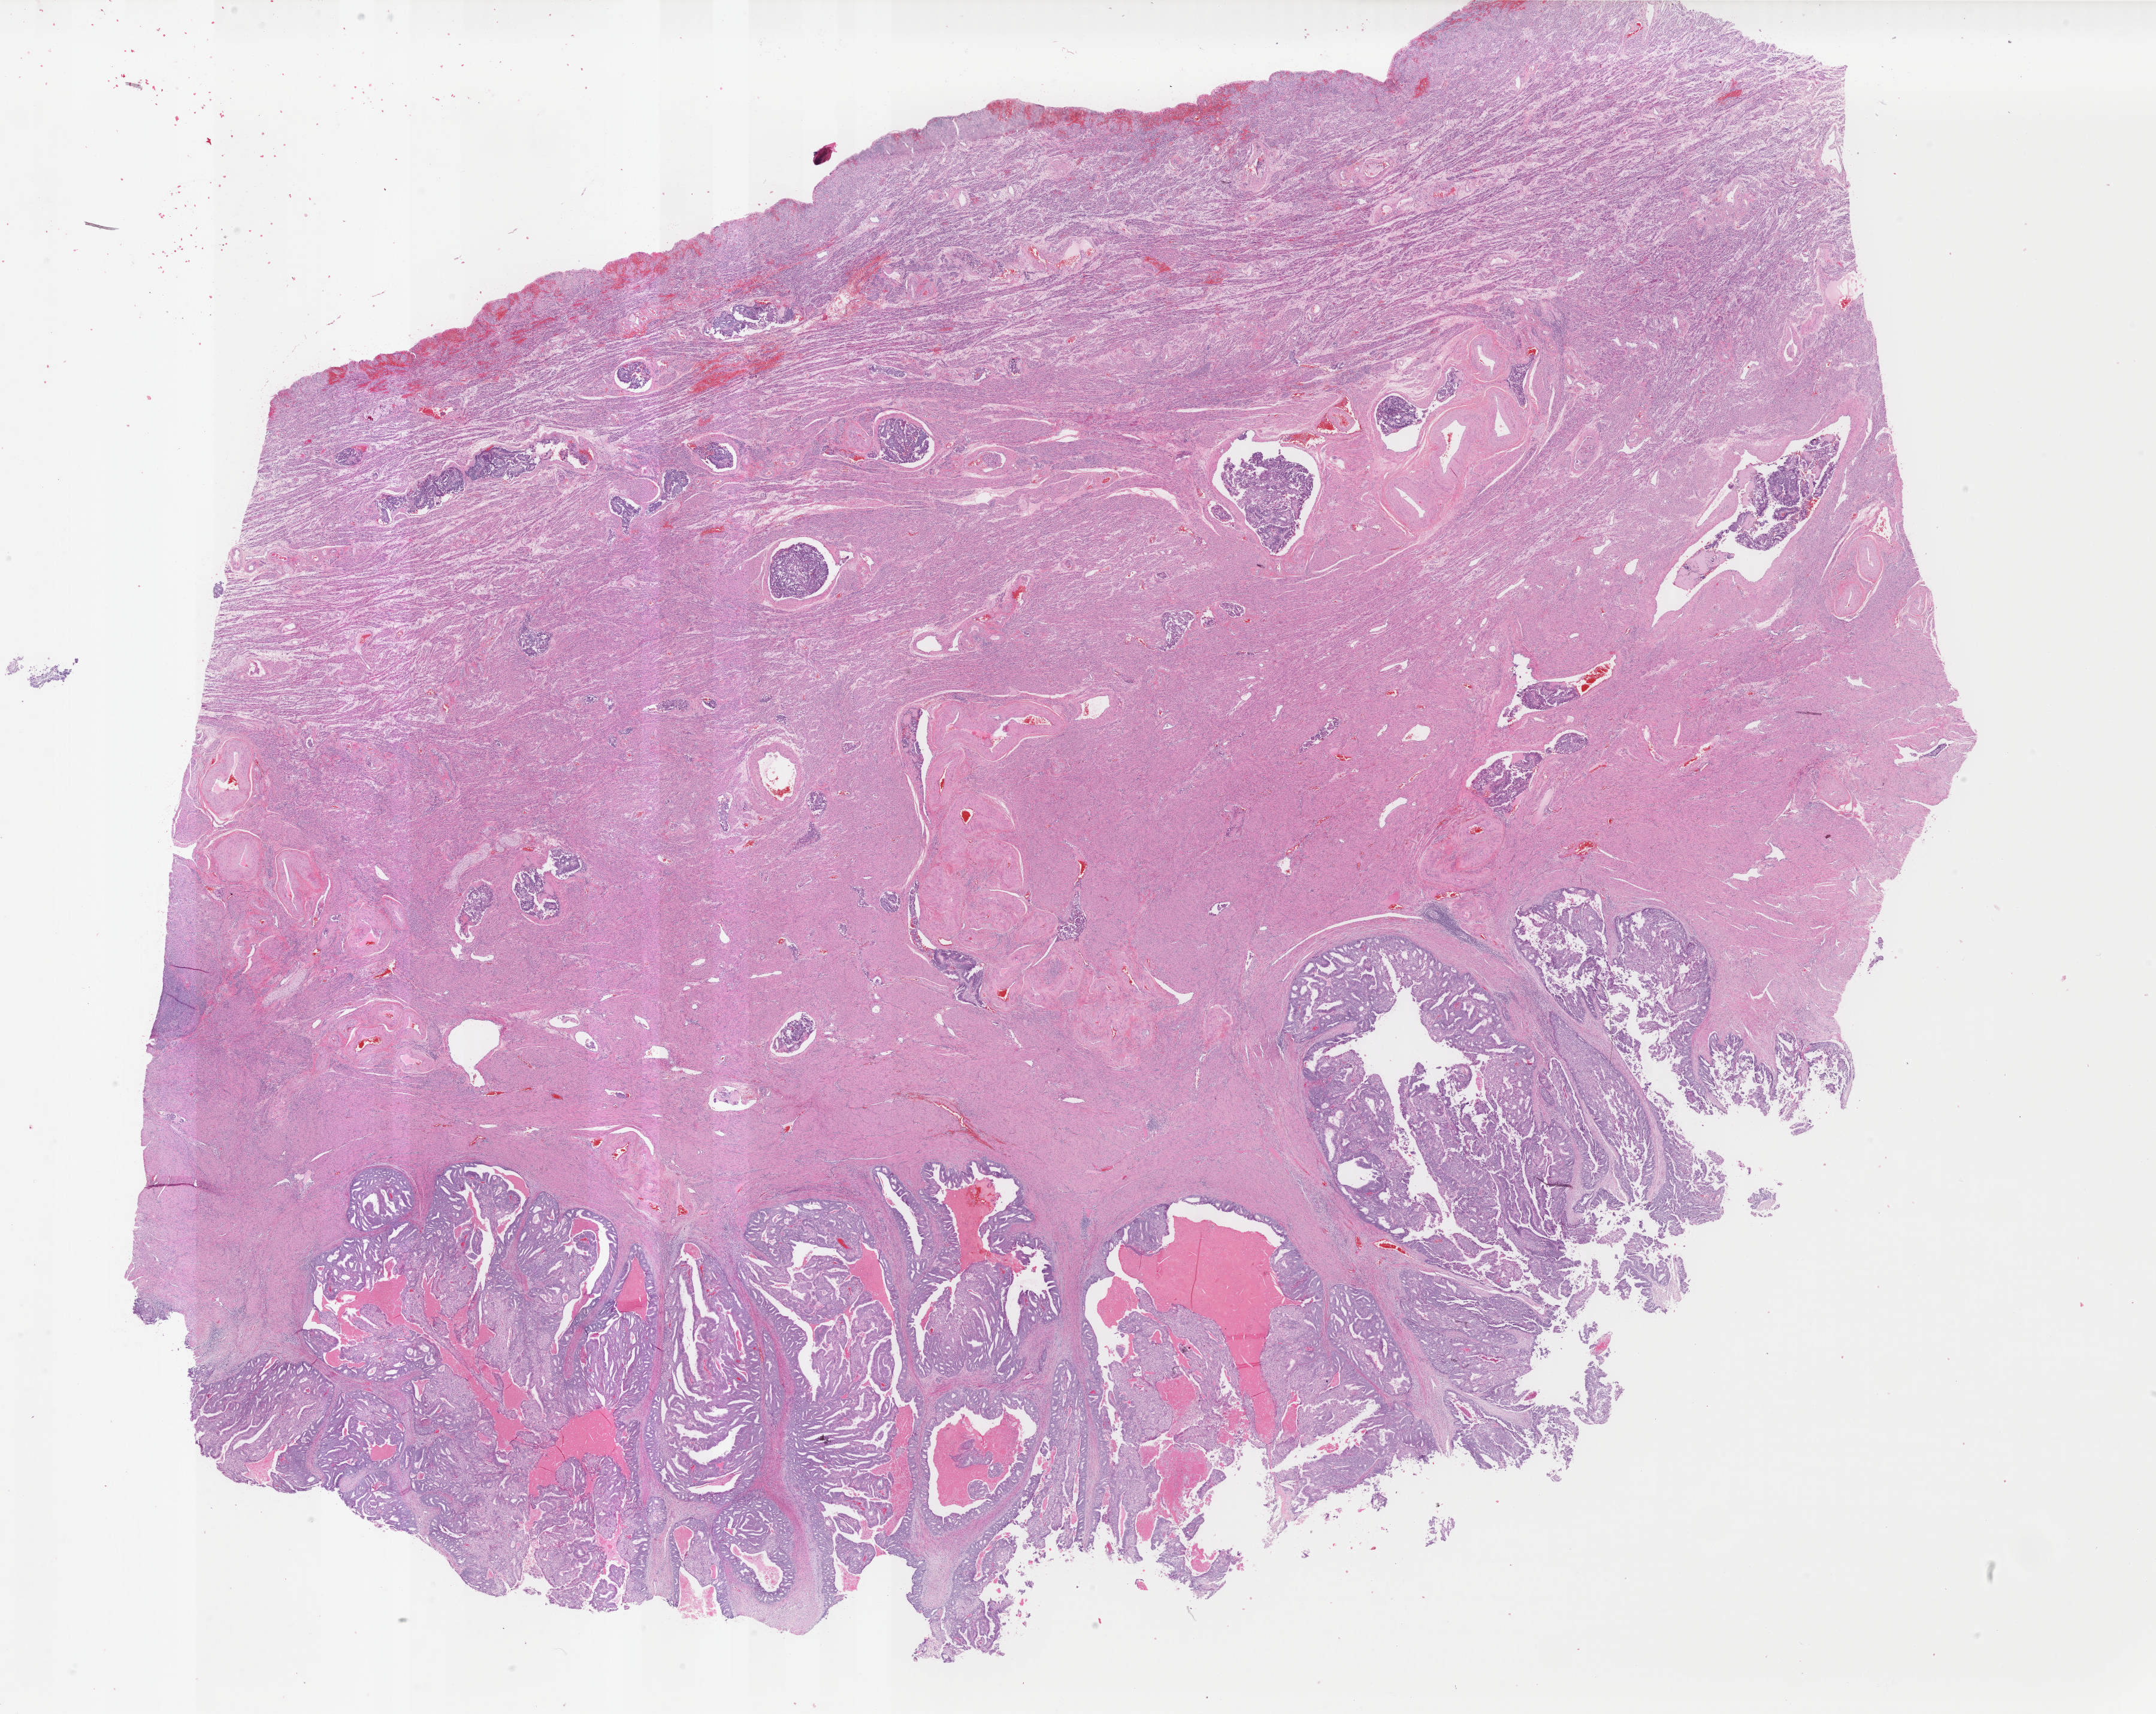
H&E-stained whole-slide image, a low-resolution overview of the entire scanned area, about 28.6 x 22.7 mm (from a 40x scan); formalin-fixed paraffin-embedded (FFPE) diagnostic section; primary tumour sample from the uterus. Patient: female, age at initial diagnosis 51 years. Histologic grade: G2 (moderately differentiated).
- FIGO stage: IB
- diagnosis: Endometrioid adenocarcinoma, NOS (endometrium)